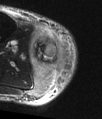
MRI of an extremity soft-tissue mass, one axial slice; position 17 of 48 along the scan axis; T2-weighted fat-saturated; MR volume resampled by the dataset authors to the PET/CT grid (not the native acquisition matrix); 3.27 mm slice thickness; 102 × 119 image matrix, field of view 100 × 116 mm. Male patient. From the clinical record (not read from this slice): histological type: pleiomorphic liposarcoma; grade: high; site of the primary tumour: right calf.
Annotated regions visible in this slice (expert contour drawn on MRI and transferred to this co-registered scan by the dataset authors):
- gross tumour volume including surrounding oedema: bounding box [x1, y1, x2, y2] px = [32, 29, 68, 95]
- gross tumour volume (mass): [35, 39, 61, 66]